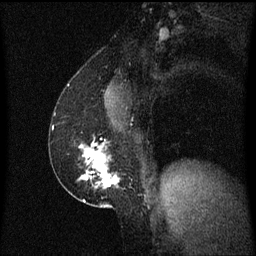
Breast MRI (dynamic contrast-enhanced), one sagittal slice; position 35 of 60 along the scan axis; dynamic contrast-enhanced series, image 2 of 3 at this slice position (ordered by acquisition); 1.5 T; TE 4.2 ms, TR 8.4 ms; 2 mm slice thickness; 256 × 256 image matrix, field of view 200 × 200 mm. Patient: female, 52 years. From the clinical record (not read from this slice): setting: breast cancer imaged before/during neoadjuvant chemotherapy; receptor status: HER2-positive.
Outlined on this slice (semi-automatic segmentation, software-assisted and operator-edited):
- analysis volume of interest (the breast-tissue region the enhancement analysis was run in; not a lesion): box from (x=62, y=138) to (x=121, y=203) px
- tumour enhancement mask (voxels above the 70 % enhancement threshold inside the analysis volume of interest): (x=80, y=144)–(x=120, y=189)